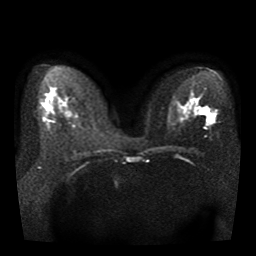
Breast MRI, one axial slice; slice 20 of 41 in the series (ordered by position); diffusion-weighted series; image 2 of 4 stored at this slice position (different b-values; order by instance number); 1.5 T; 256 × 256 image matrix, field of view 330 × 330 mm. Female patient.
Annotated regions visible in this slice (manually delineated by an expert):
- tumour on diffusion-weighted imaging: bounding box (x1, y1, x2, y2) in pixels: (206, 110, 215, 119)